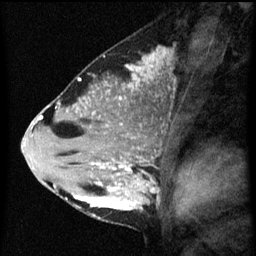
Breast MRI (dynamic contrast-enhanced), one sagittal slice. Position 28 of 60 along the scan axis. Dynamic contrast-enhanced series, image 2 of 3 at this slice position (ordered by acquisition). 1.5 T. TE 4.2 ms, TR 8 ms. 2.3 mm slice thickness. 256 × 256 image matrix. Patient: female, 33 years.
Outlined on this slice (semi-automatic segmentation, software-assisted and operator-edited):
- analysis volume of interest (the breast-tissue region the enhancement analysis was run in; not a lesion): bounding box <71,118,162,217> (left, top, right, bottom; pixels)
- tumour enhancement mask (voxels above the 70 % enhancement threshold inside the analysis volume of interest): <74,160,154,211>